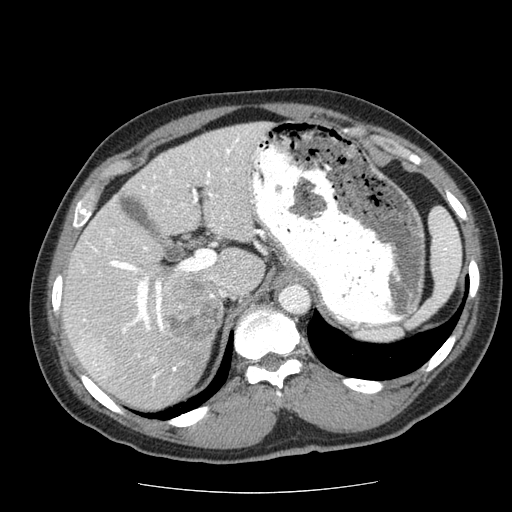
Contrast-enhanced abdominal CT (liver protocol), one axial slice. Slice 39 of 85 in the series (ordered by position). Reconstruction kernel STANDARD. 120 kVp. Soft-tissue window (W 400 / L 40 HU). 2.5 mm slice thickness. 512 × 512 image matrix, field of view 360 × 360 mm. From the clinical record (not read from this slice): diagnosis: hepatocellular carcinoma (patient treated with transarterial chemoembolisation; whether this scan precedes or follows treatment is not stated here); TNM stage (as recorded): Stage-IIIA; Child-Pugh class: A; tumour differentiation: well differentiated.
Annotated regions visible in this slice (semi-automatic segmentation, software-assisted and operator-edited):
- abdominal aorta: box from (x=278, y=284) to (x=309, y=314) px
- liver parenchyma outside the tumour (the mass and vessels are separate outlines, so this box may not span the whole liver): (x=64, y=122)–(x=270, y=408)
- mass: (x=161, y=273)–(x=222, y=340)
- liver vessels: (x=77, y=136)–(x=240, y=385)